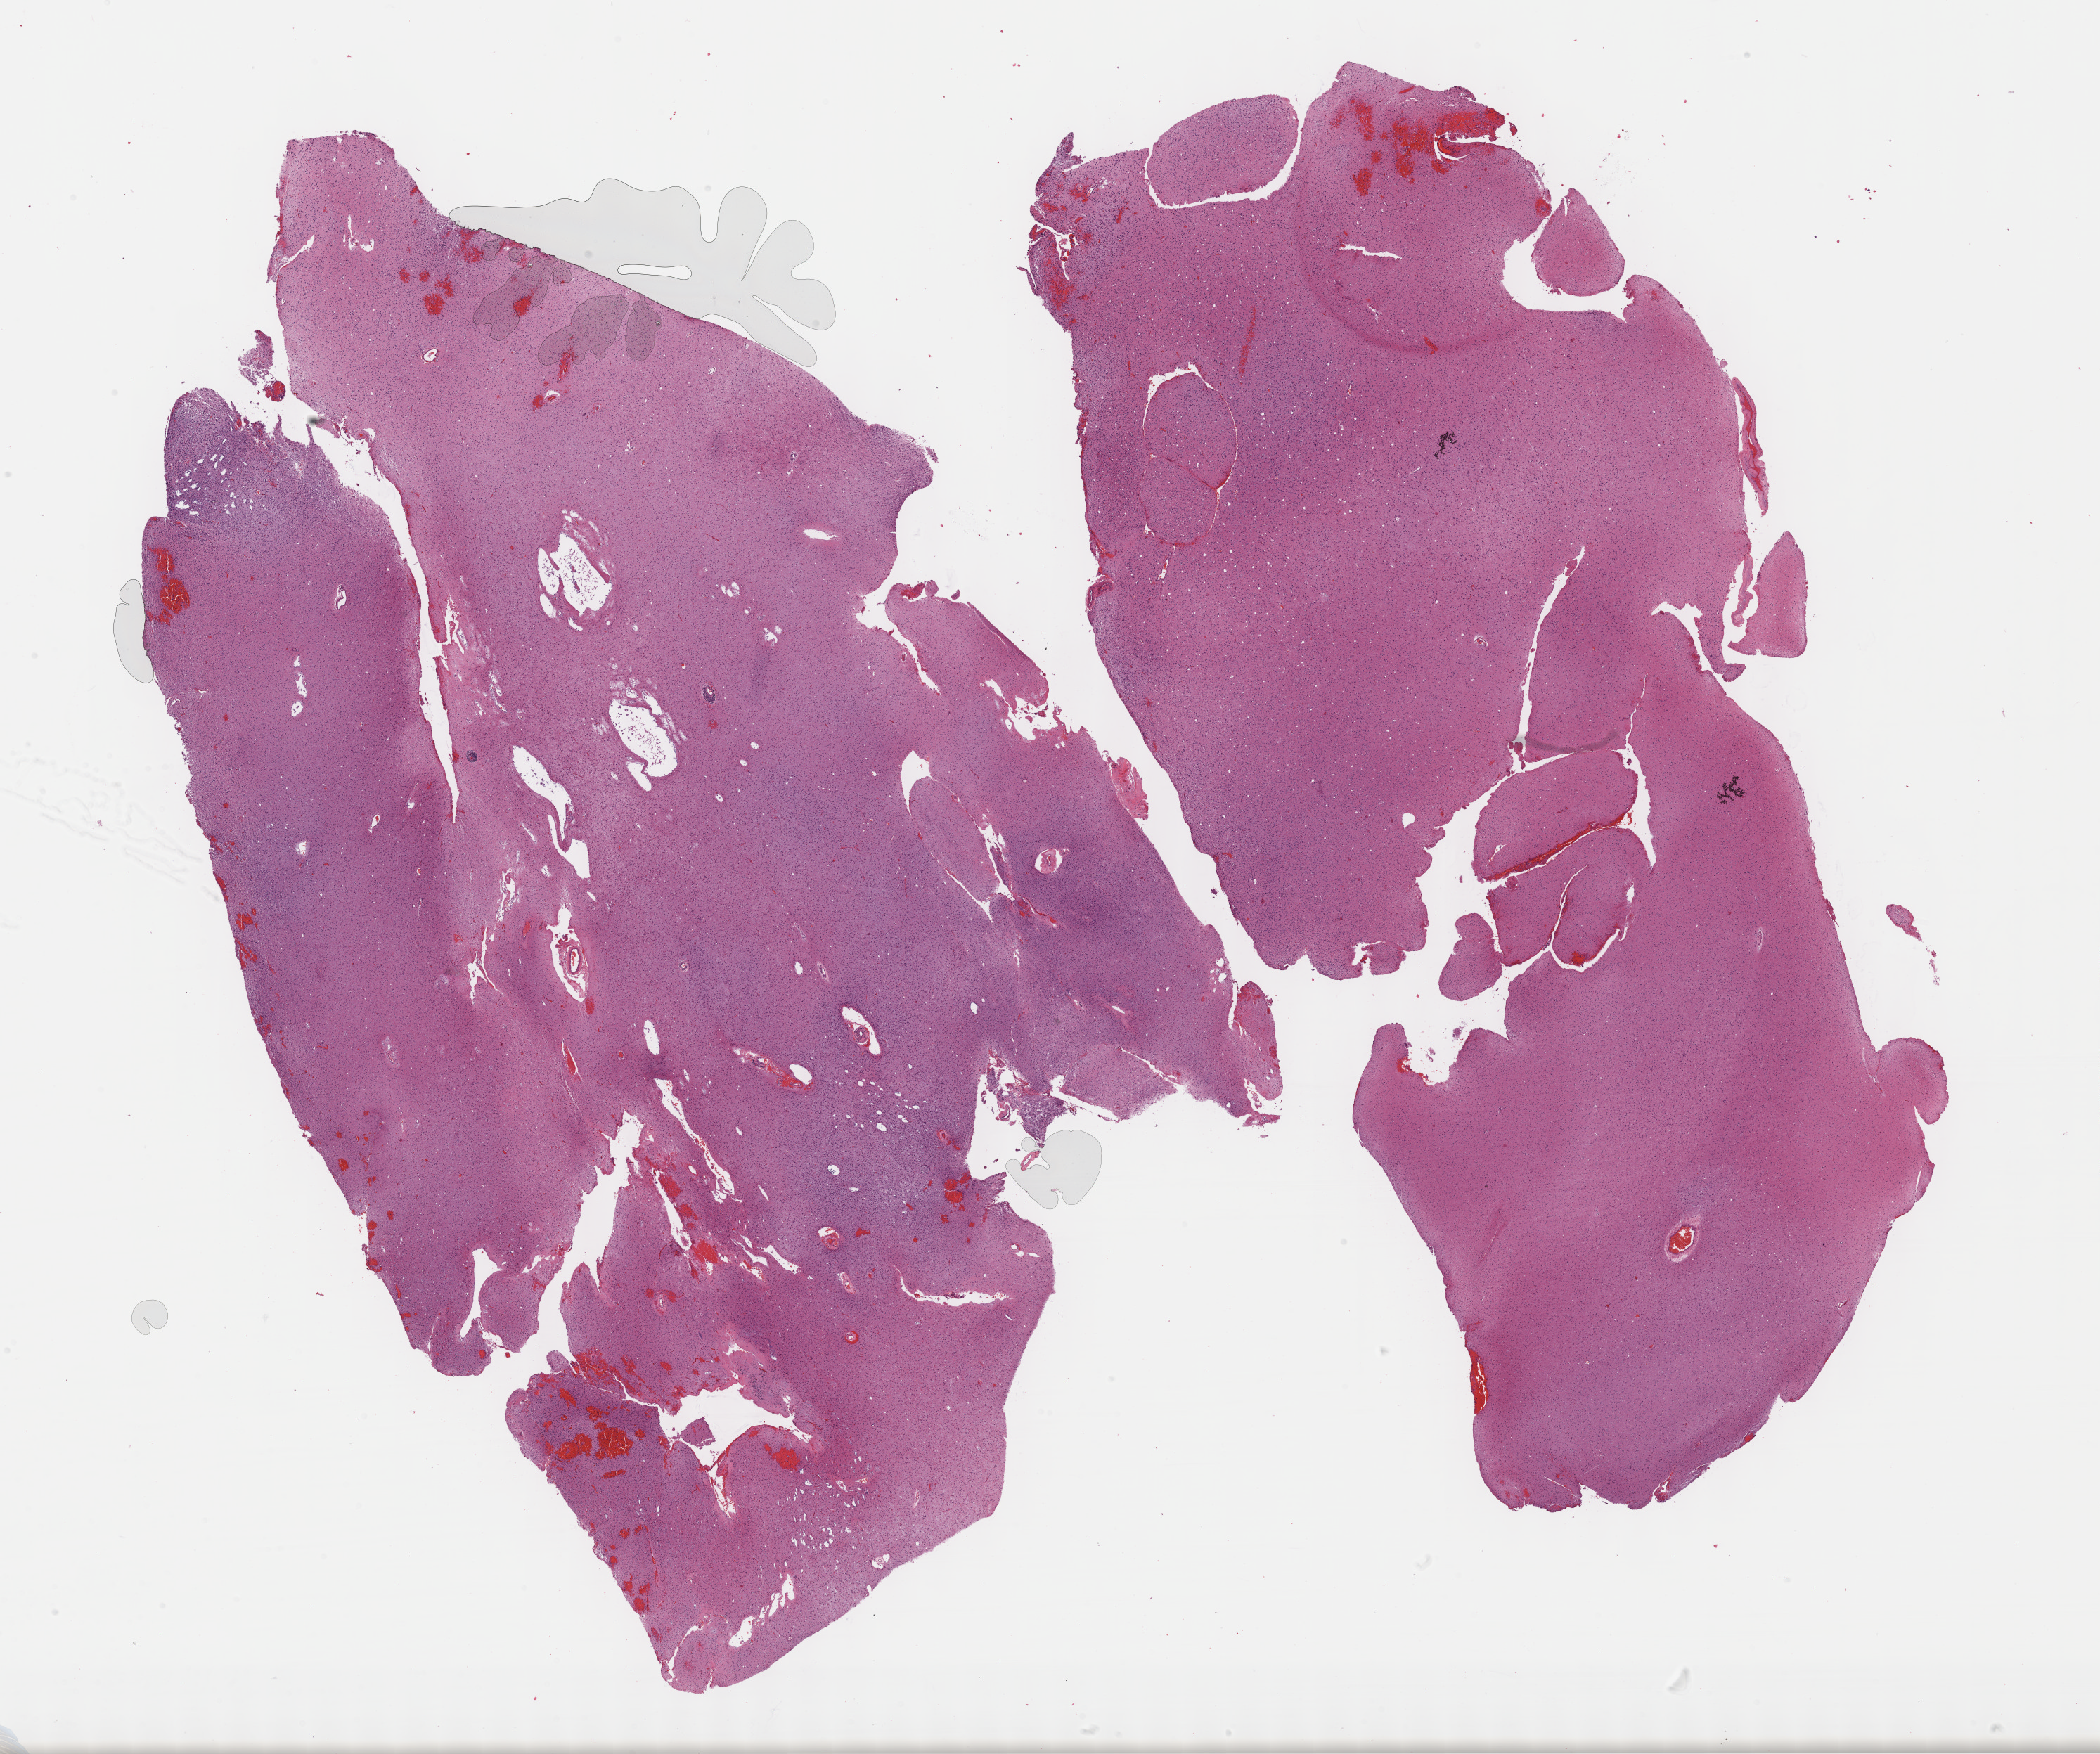
Whole-slide histology image, Hematoxylin and eosin (H&E) stained, whole scanned area (about 24.2 x 20.2 mm) shown as a low-resolution overview, FFPE section, sample: primary tumour, brain. Male patient; age at initial diagnosis 29 years. Histologic grade: G2 (moderately differentiated).
- diagnosis: Oligodendroglioma, NOS